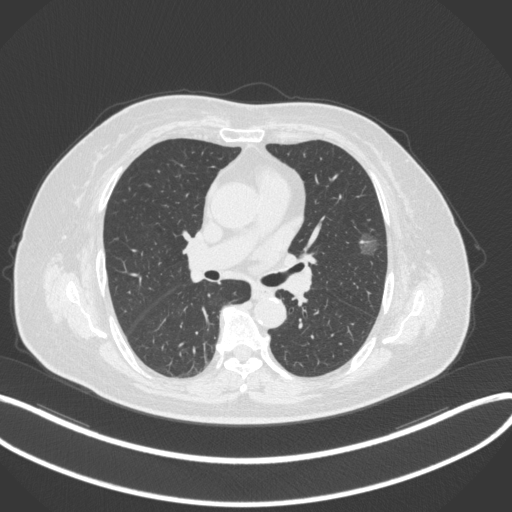
Chest CT, one axial slice; slice 176 of 286 in the series (ordered by position); 120 kVp; lung window (W 1500 / L -600 HU); 1 mm slice thickness; 512 × 512 image matrix, field of view 400 × 400 mm. Patient: female, 76 years. From the clinical record (not read from this slice): clinical TNM (as recorded): T1b N0 M0; histopathological grade: G1-2.
Annotated regions visible in this slice (bounding box drawn by a radiologist):
- lung tumour (recorded histology: adenocarcinoma): bounding box (x1, y1, x2, y2) in pixels: (354, 228, 380, 261)